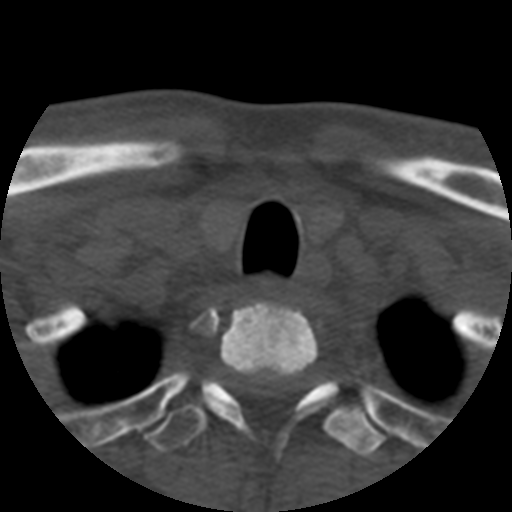
CT including the spine, one axial slice. Slice 441 of 508 in the series (ordered by position). 120 kVp. Bone window (W 1800 / L 400 HU). 512 × 512 image matrix, field of view 160 × 160 mm. Patient age 57 years. From the clinical record (not read from this slice): primary cancer: prostate.
Annotated regions visible in this slice (semi-automatic segmentation, software-assisted and operator-edited):
- T1 vertebra: box from (x=145, y=301) to (x=337, y=447) px
- T2 vertebra: (x=146, y=379)–(x=385, y=460)